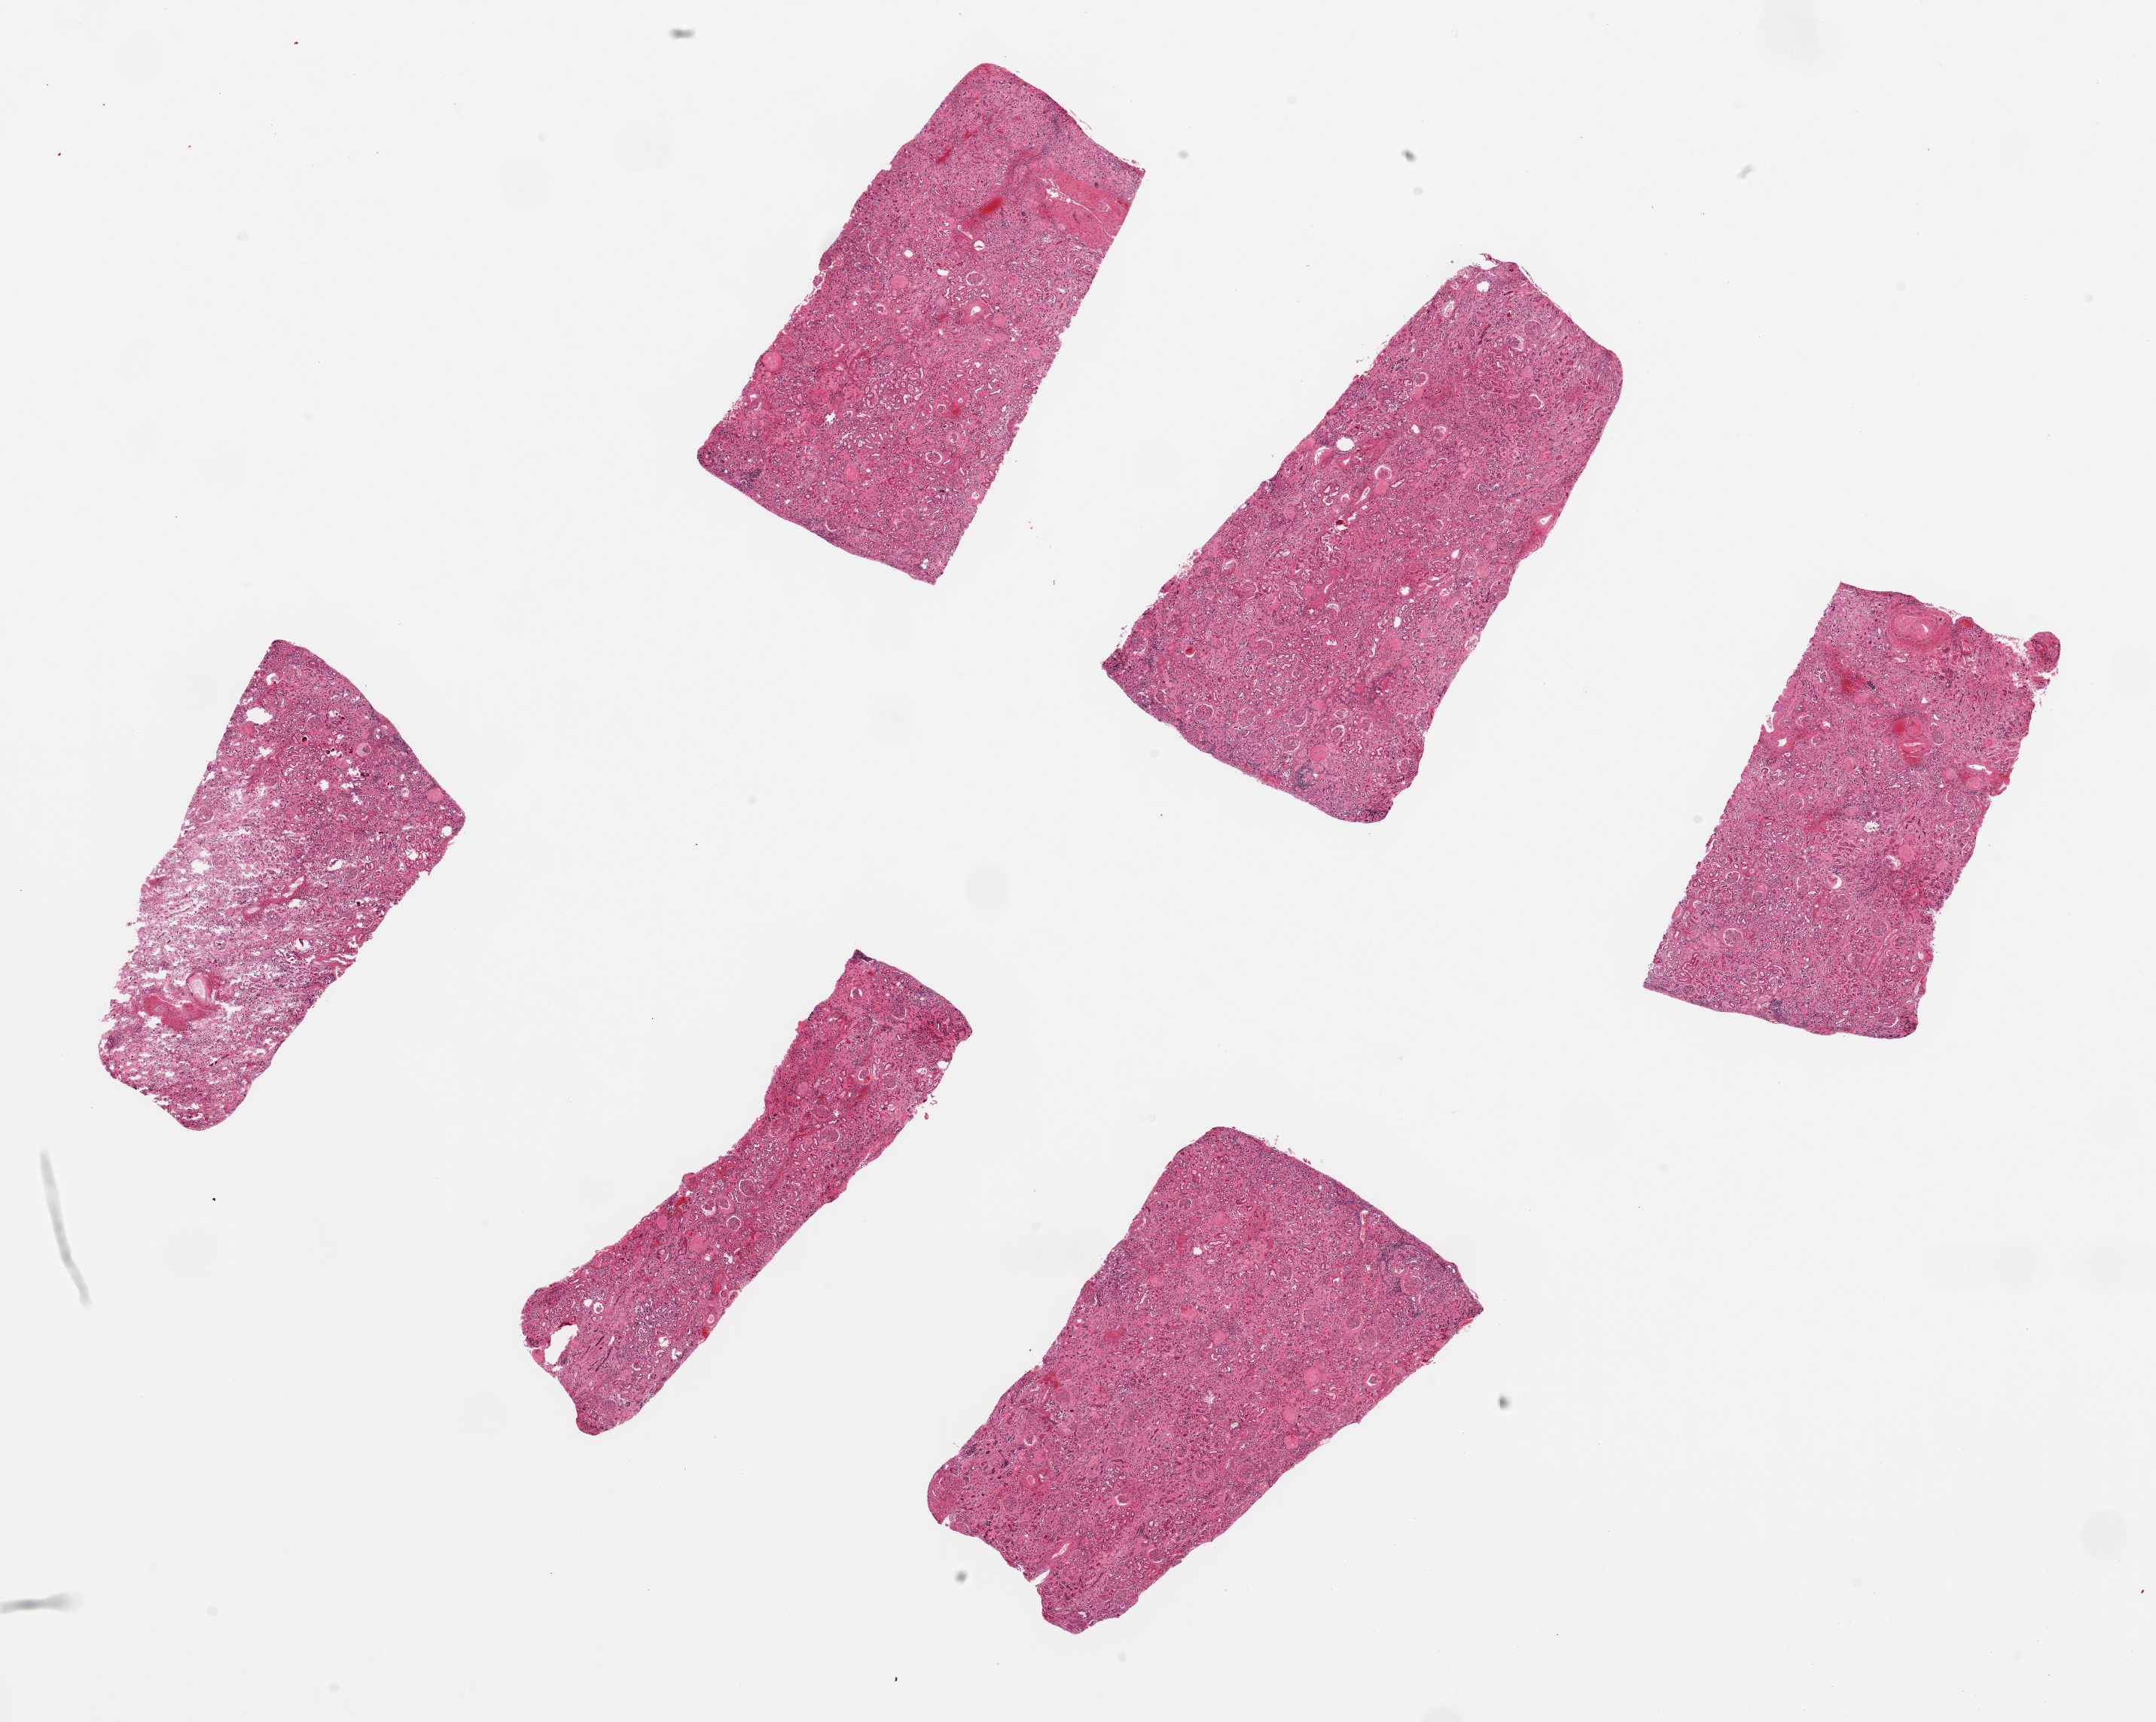
Whole-slide image, H&E stain — a low-resolution overview of the entire scanned area, about 22.6 x 18.1 mm (from a 20x scan); PAXgene-fixed, paraffin-embedded tissue; sampled site (target tissue): renal cortex; donor tissue sample. Donor: male.
Pathologist's review note for this sample: 6 pieces ~5x3.5mm.